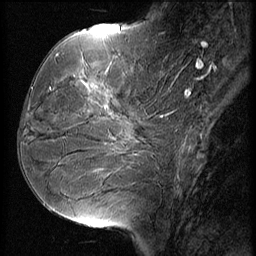
Breast MRI (dynamic contrast-enhanced), one sagittal slice; position 21 of 56 along the scan axis; 3 images stored at this slice position (order not interpretable as contrast timing); 1.5 T; TE 4.2 ms, TR 9 ms; 256 × 256 image matrix, field of view 180 × 180 mm. Patient: female, 51 years. From the clinical record (not read from this slice): setting: breast cancer imaged before/during neoadjuvant chemotherapy; receptor status: HR-positive, HER2-negative.
Structures marked on this image (semi-automatically segmented with operator editing):
- analysis volume of interest (the breast-tissue region the enhancement analysis was run in; not a lesion): box from (x=23, y=56) to (x=156, y=165) px
- tumour enhancement mask (voxels above the 140 % enhancement threshold inside the analysis volume of interest): (x=78, y=60)–(x=118, y=119)